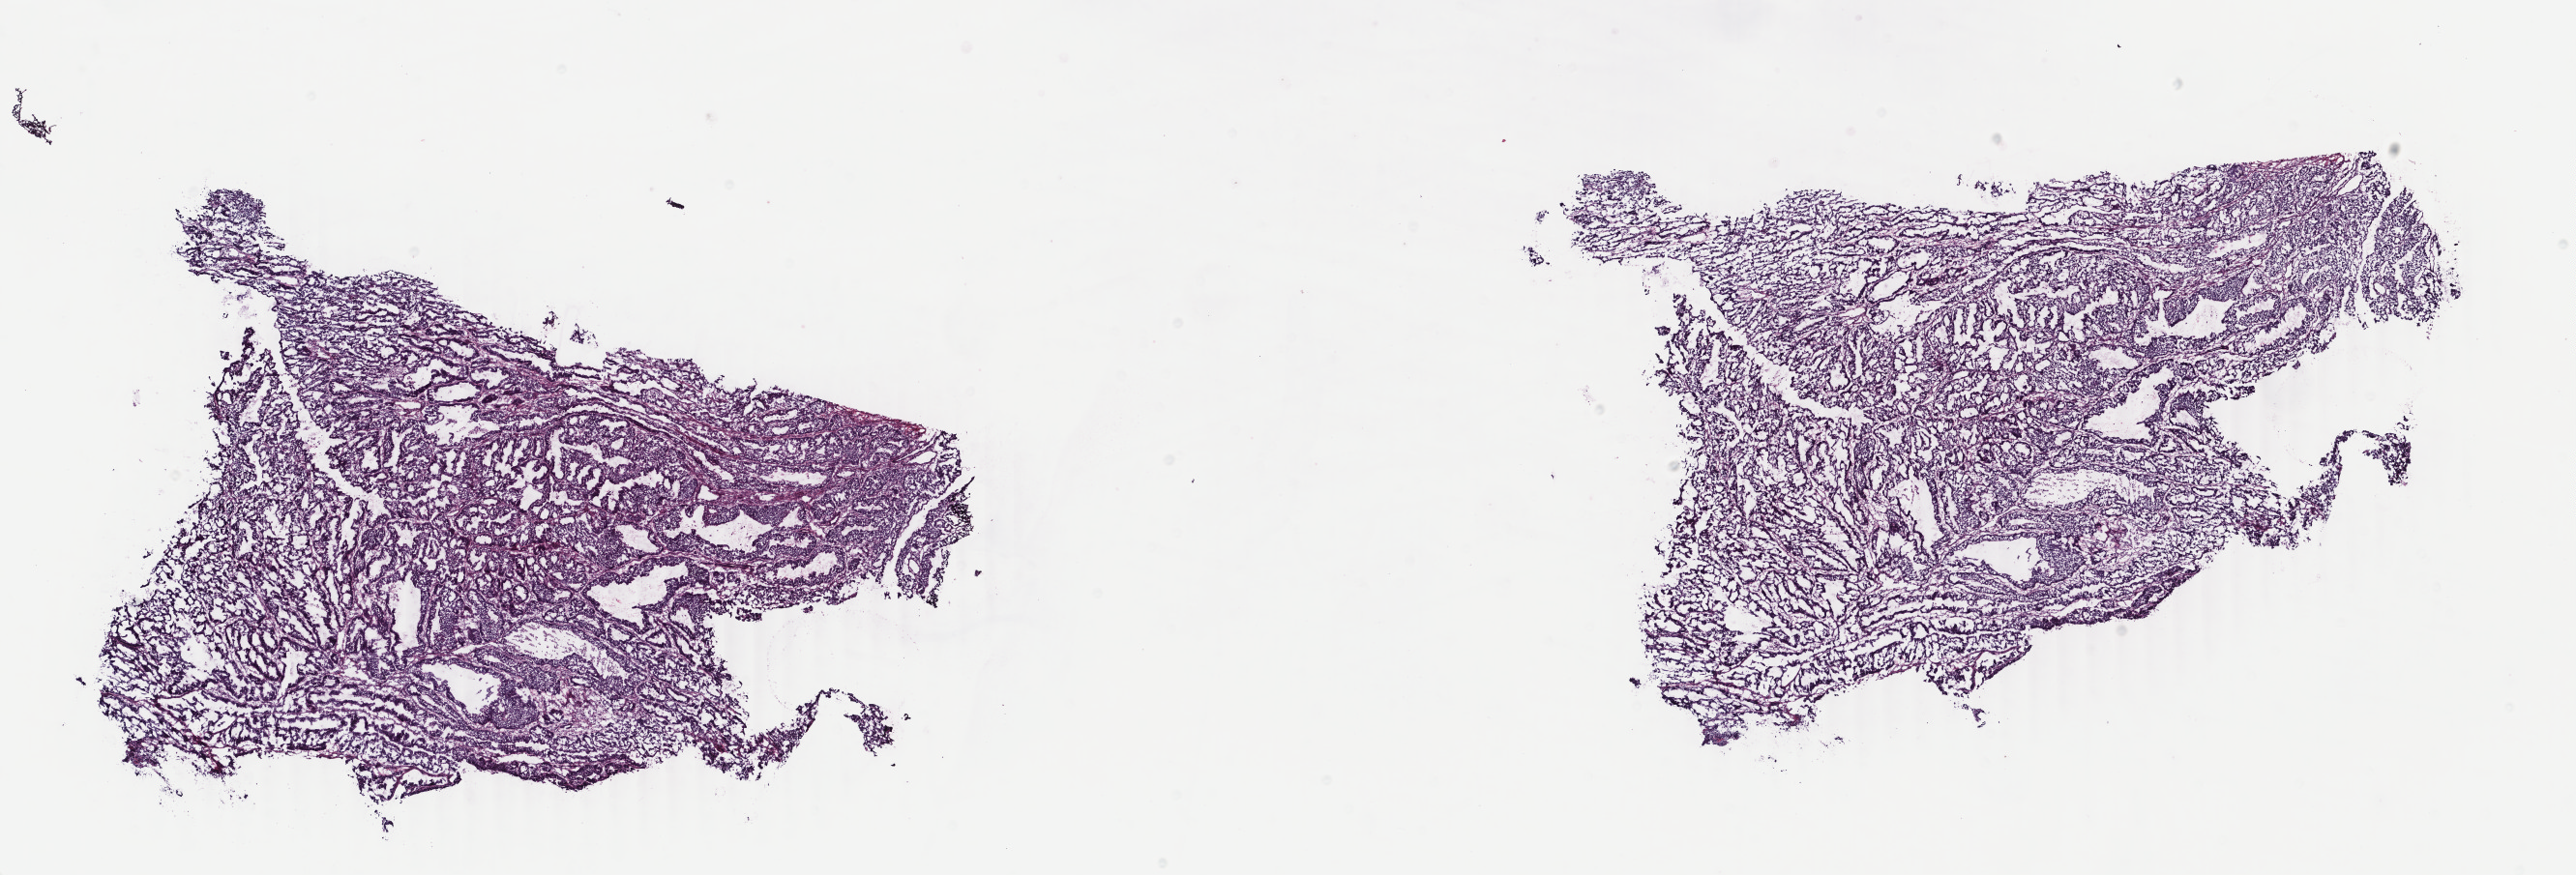
Hematoxylin and eosin (H&E) stained whole-slide image — a low-resolution overview of the entire scanned area, about 21.2 x 7.2 mm. Frozen section from the bottom of the tissue portion. Uterus, primary tumour sample. Female patient; age at initial diagnosis 39 years. Histologic grade: G1 (well differentiated). Pathologist review of this section (percent, as recorded): tumour cells 100%, tumour nuclei 90%, normal cells 0%, stromal cells 0%, necrosis 0%. Infiltration values recorded for this section: lymphocyte infiltration 0%, monocyte infiltration 0%, neutrophil infiltration 0%.
* pathologic diagnosis: Endometrioid adenocarcinoma, NOS (endometrium)
* lymph nodes positive (case pathology): 0 of 16 examined
* FIGO stage: IA